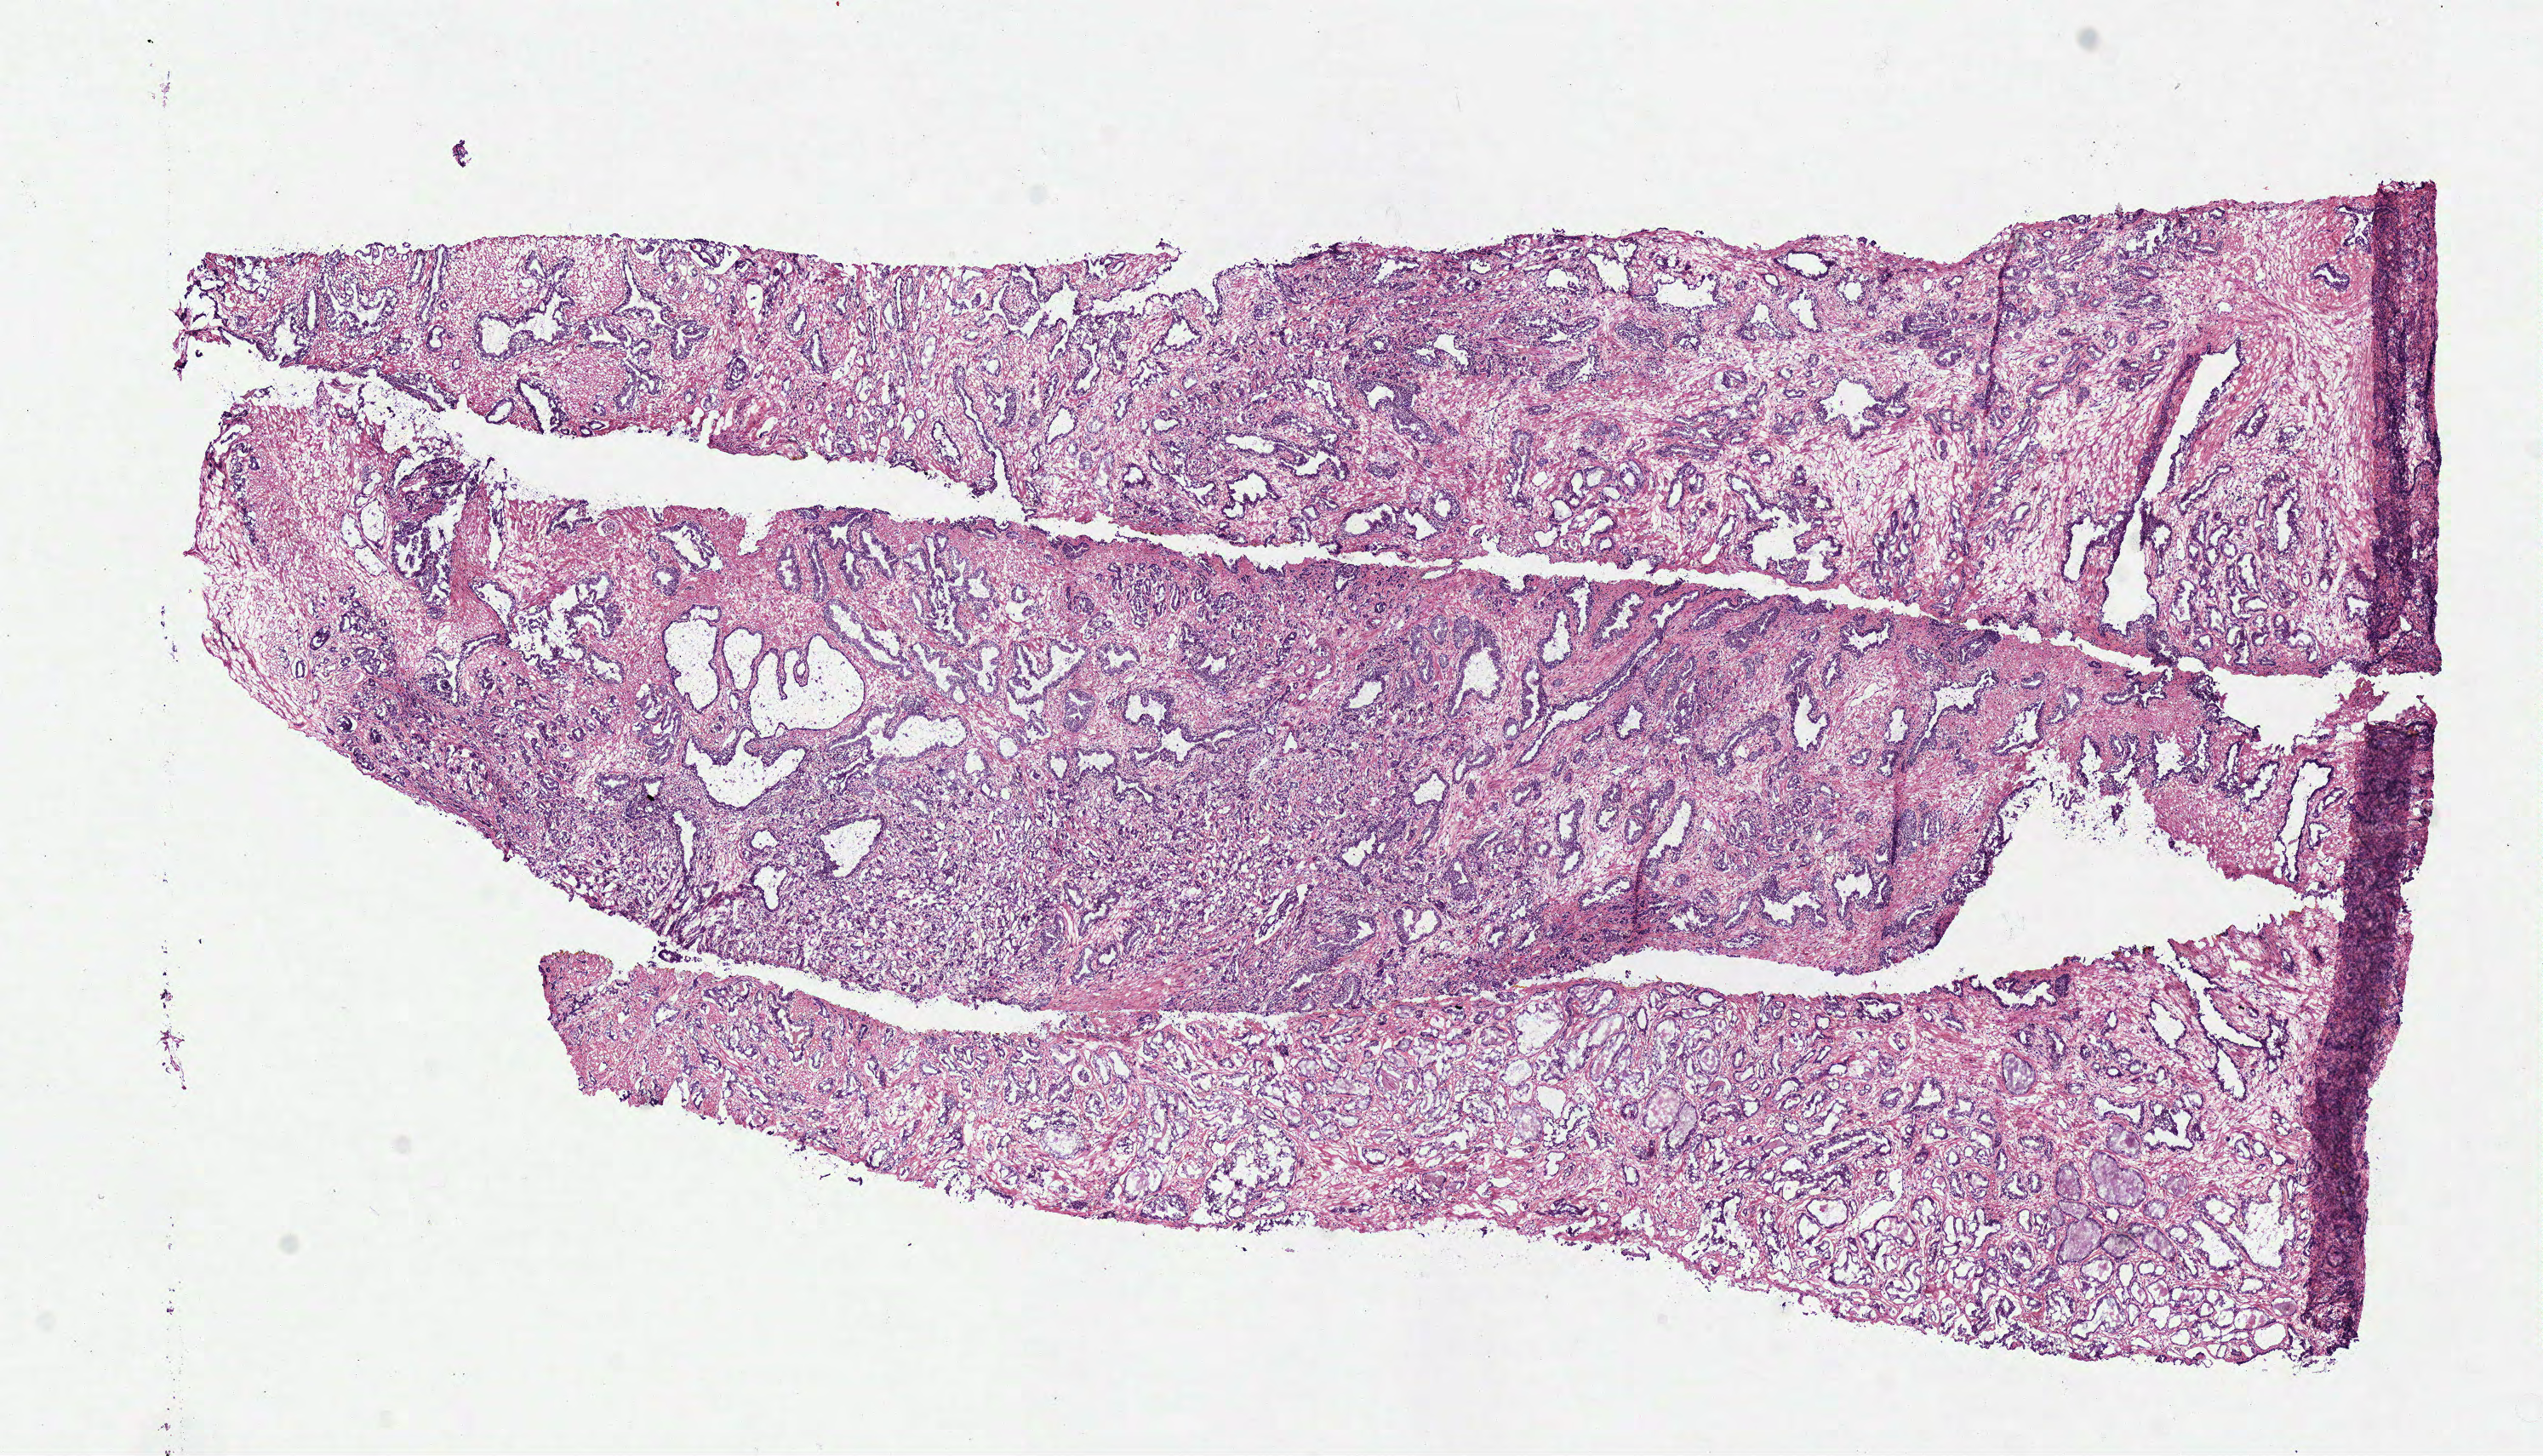
Whole-slide histology image, Hematoxylin and eosin (H&E) stained — shown as a low-resolution overview of the whole scanned area (about 11.7 x 6.7 mm, from a 40x scan). Frozen section from the top of the tissue portion. Prostate, primary tumour sample. Male patient; age at initial diagnosis 60 years. Gleason score: 9 (4+5). Pathologist review of this section (percent, as recorded): tumour cells 55%, tumour nuclei 60%, normal cells 30%, stromal cells 15%, necrosis 0%. Inflammatory infiltration, as recorded: lymphocyte infiltration 2%, monocyte infiltration 0%, neutrophil infiltration 0%.
Laterality: bilateral. Histologic diagnosis: Acinar cell carcinoma (prostate gland). Lymph nodes positive (case pathology): 0 of 5 examined.